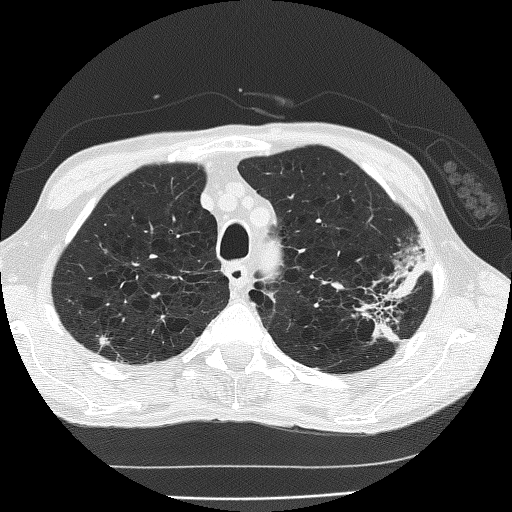
Axial slice from a low-dose chest CT screening exam. Second screening round (one year after baseline). Lung window (W 1500 / L -600 HU). Lung (sharp) reconstruction kernel (FC51). Slice 39 of 185 in the series. Male participant, aged 60 years at enrolment. Current smoker at enrolment.
Expert reader's lesion annotation, bounding box [x1, y1, x2, y2] px = [346, 256, 431, 339]. The screening reader recorded 2 non-calcified nodules or masses ≥4 mm on this exam (left upper lobe, left upper lobe); which of them this box marks is not recorded. Participant outcome: lung cancer diagnosed 178 days after this screen — bronchiolo-alveolar carcinoma, mucinous, left upper lobe, stage IV (AJCC 6th edition).